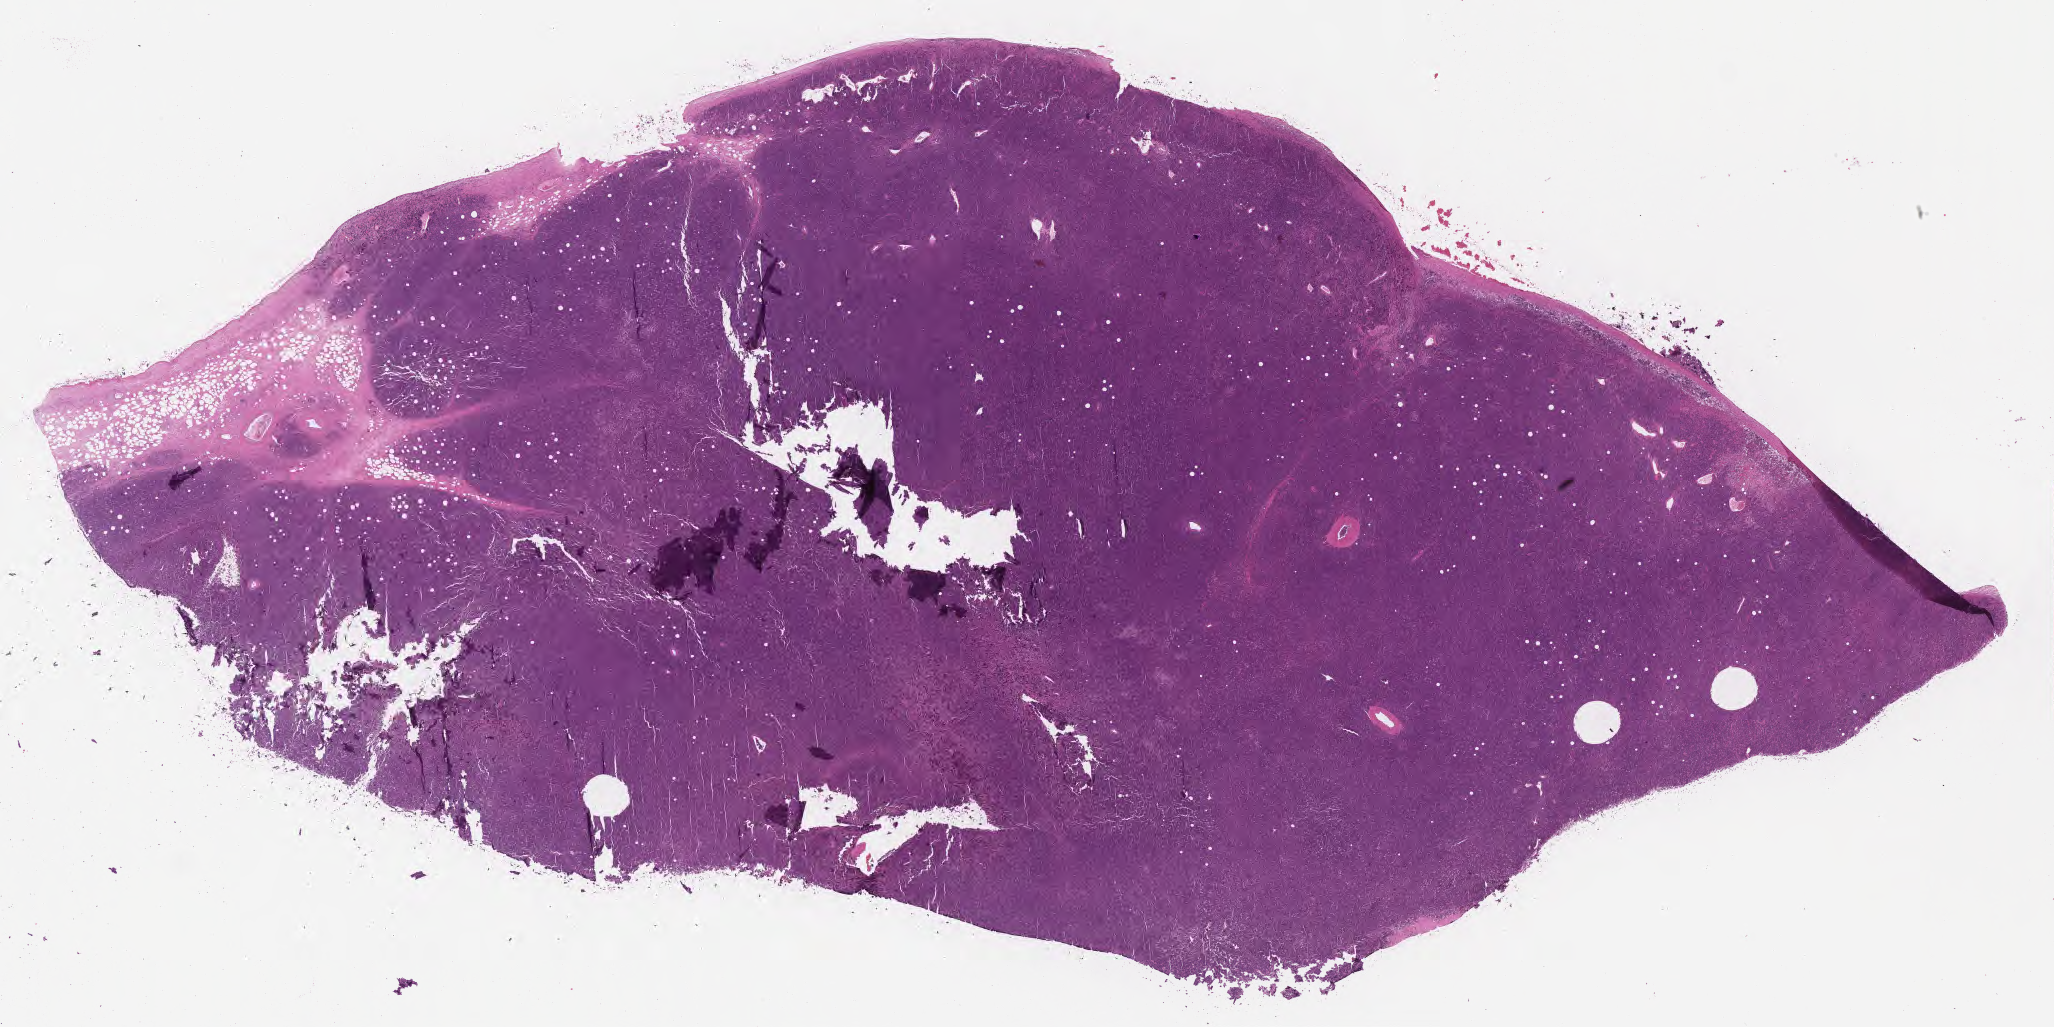
Whole-slide image, haematoxylin and eosin stain — whole scanned area (about 33.2 x 16.6 mm) shown as a low-resolution overview; FFPE section; primary tumor. Patient male; 51 years old. Pathologist review of this section (percent, as recorded): tumor cells 90%, tumor nuclei 95%, stromal cells 5%, necrosis 5%, normal cells 0%. Infiltration values recorded for this section: lymphocyte infiltration 40%, monocyte infiltration 35%, neutrophil infiltration 5%.
Section: top of the tissue portion. Histologic diagnosis: Burkitt lymphoma, NOS. Ann Arbor stage (patient): Stage IV.